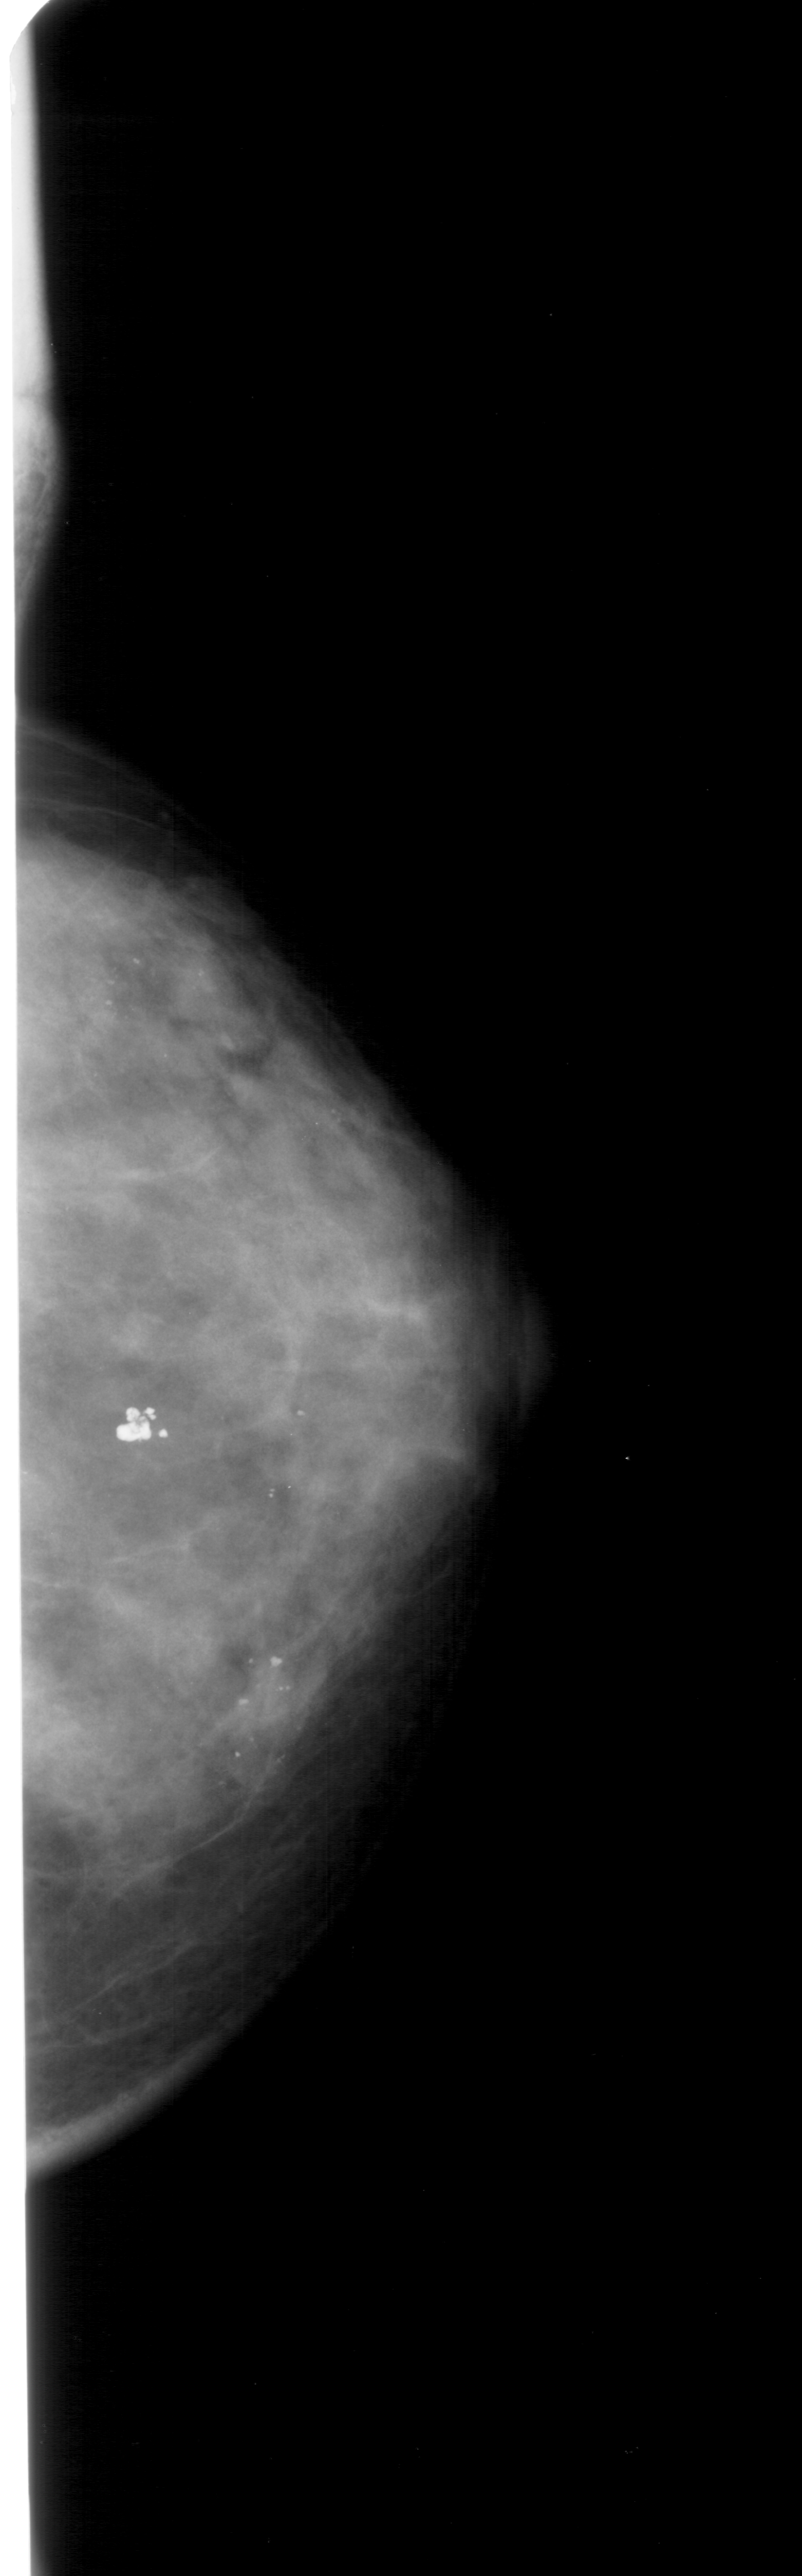
Digitized screen-film mammogram; right breast; CC view; 802 × 2576 image matrix.
Expert-marked regions of interest on this image (one box per marked abnormality):
- calcifications, morphology pleomorphic, distribution clustered; BI-RADS assessment category 4; pathology result (as recorded, not read from the image): malignant: bounding box [x1, y1, x2, y2] px = [80, 934, 233, 1095]